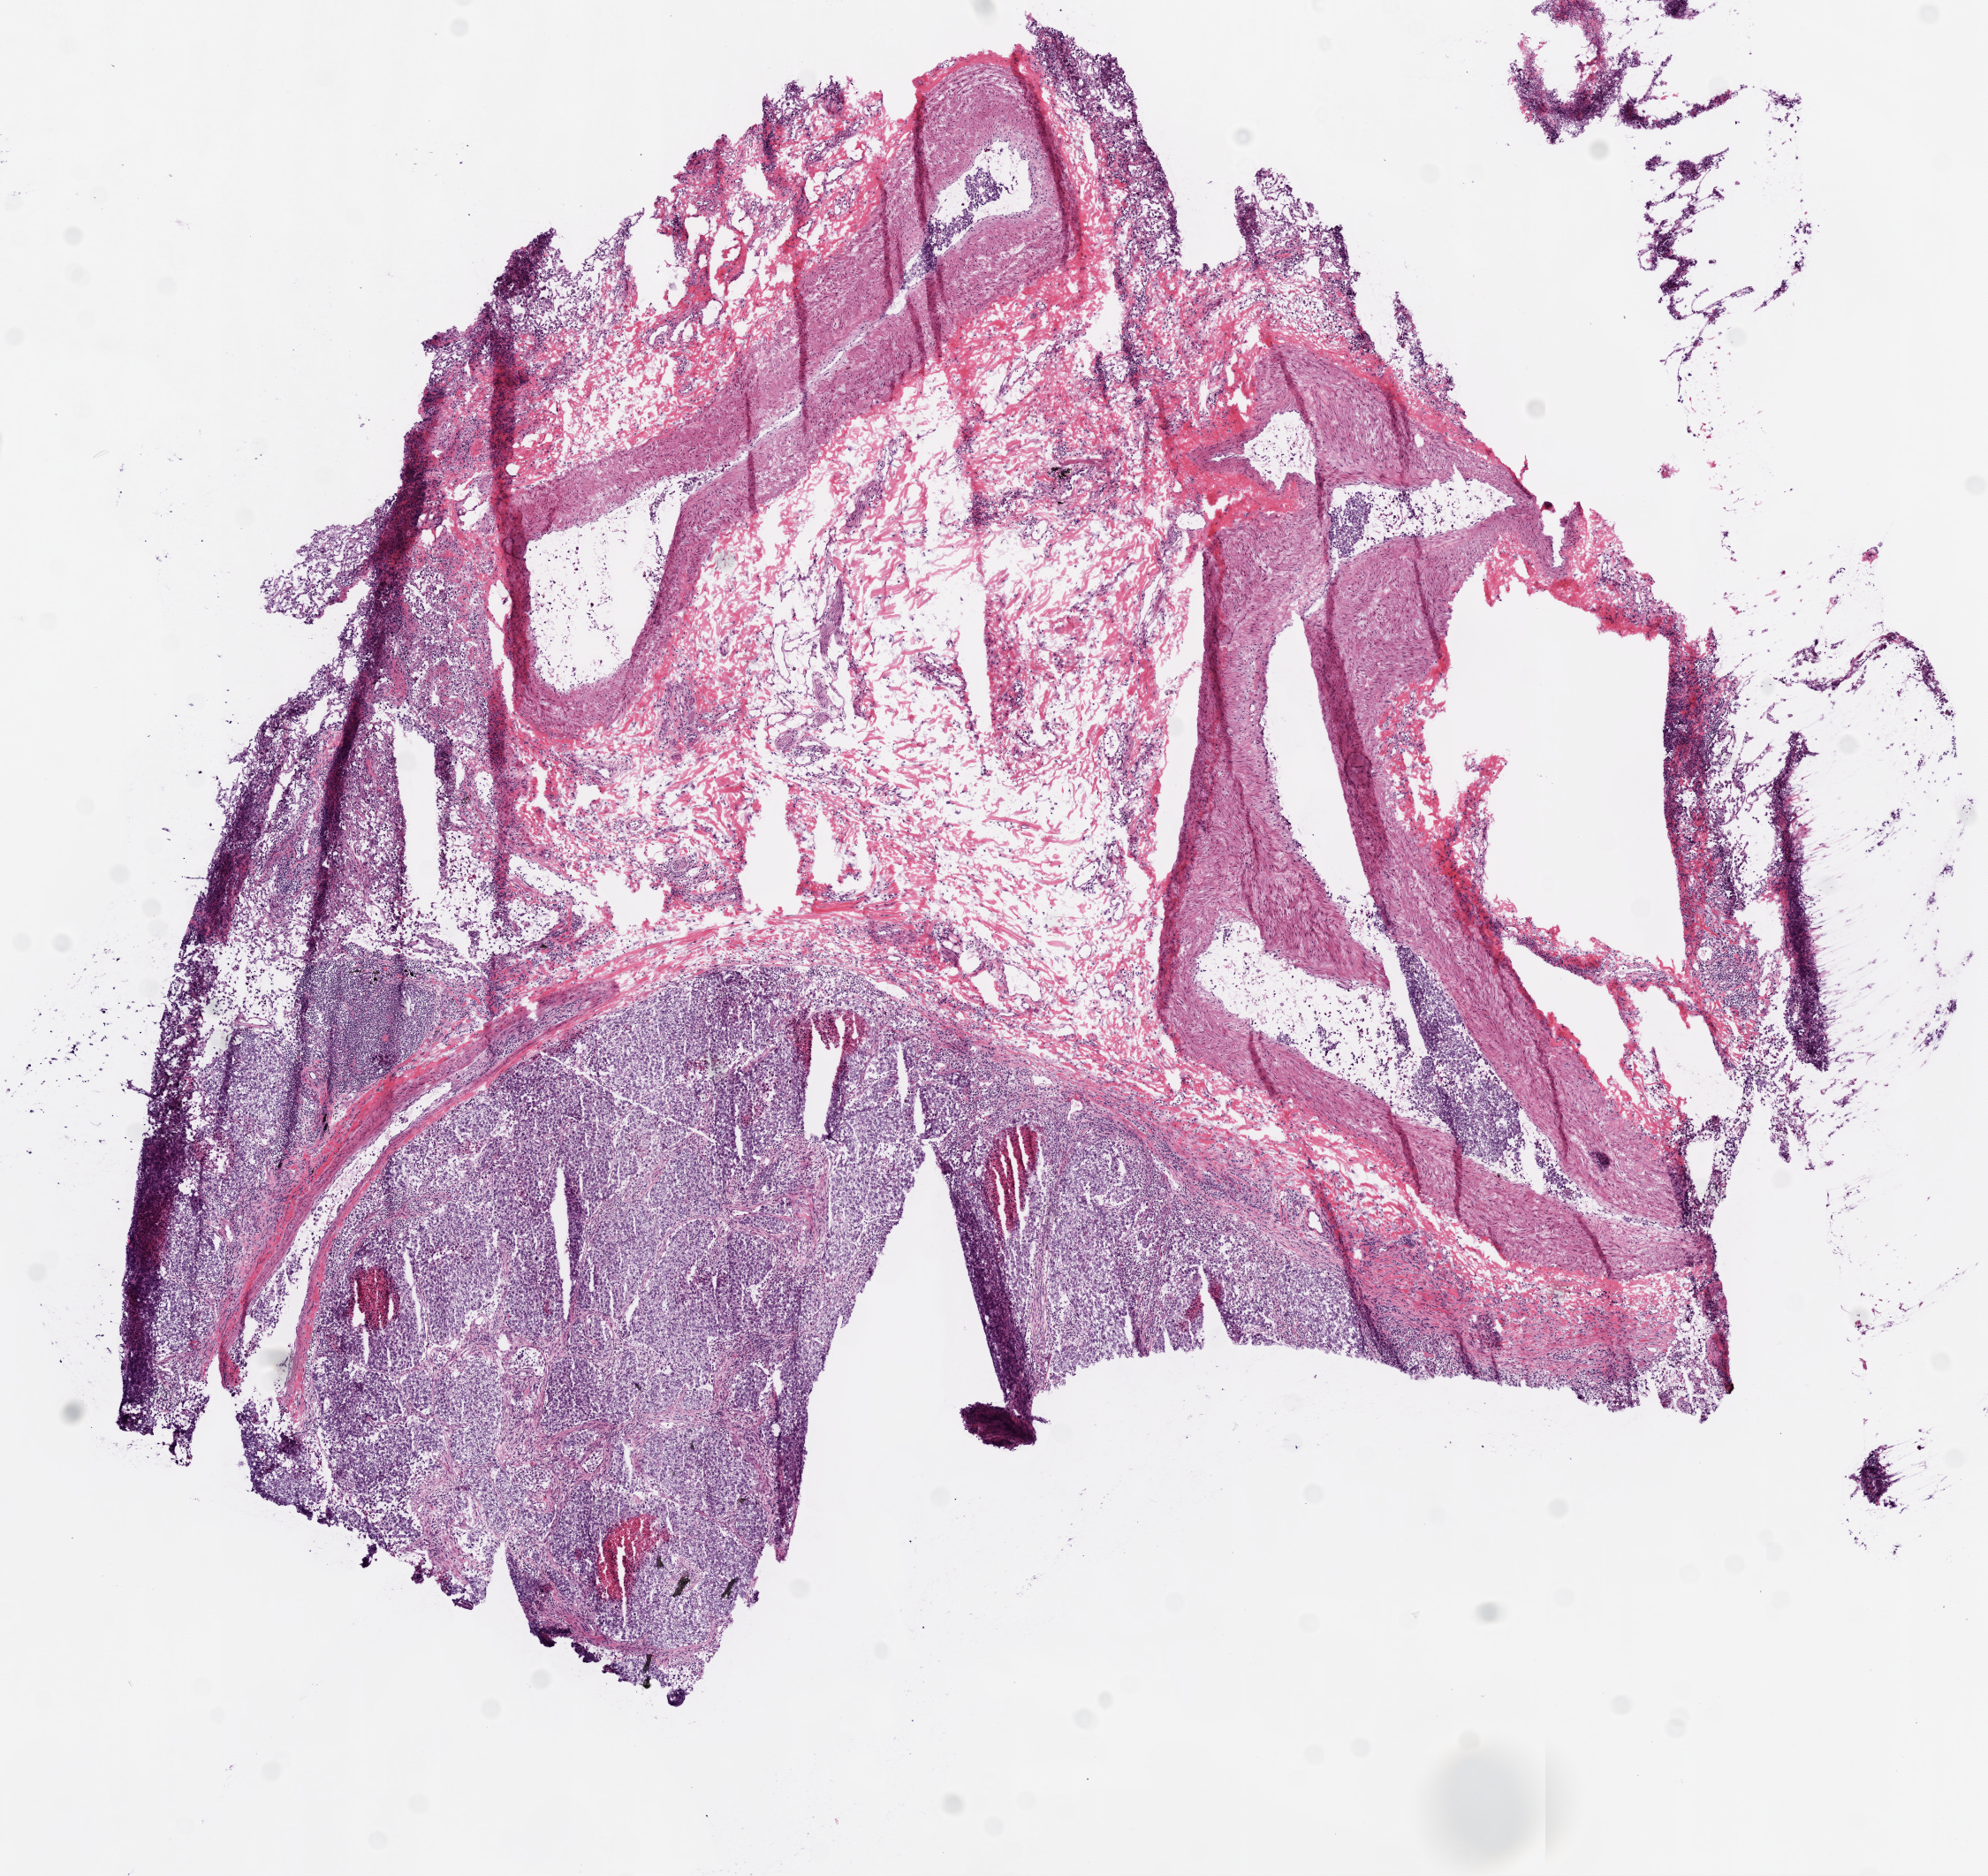
Whole-slide histology image, H&E-stained — shown as a low-resolution overview of the whole scanned area (about 9.0 x 8.5 mm, from a 20x scan), frozen section, lung, primary tumour sample. Patient: male, age at initial diagnosis 58 years. Pathologist review of this section (percent, as recorded): tumour cells 65%, tumour nuclei 85%, normal cells 0%, stromal cells 15%, necrosis 20%.
AJCC pathologic stage: IA. Histologic diagnosis: Squamous cell carcinoma, NOS.